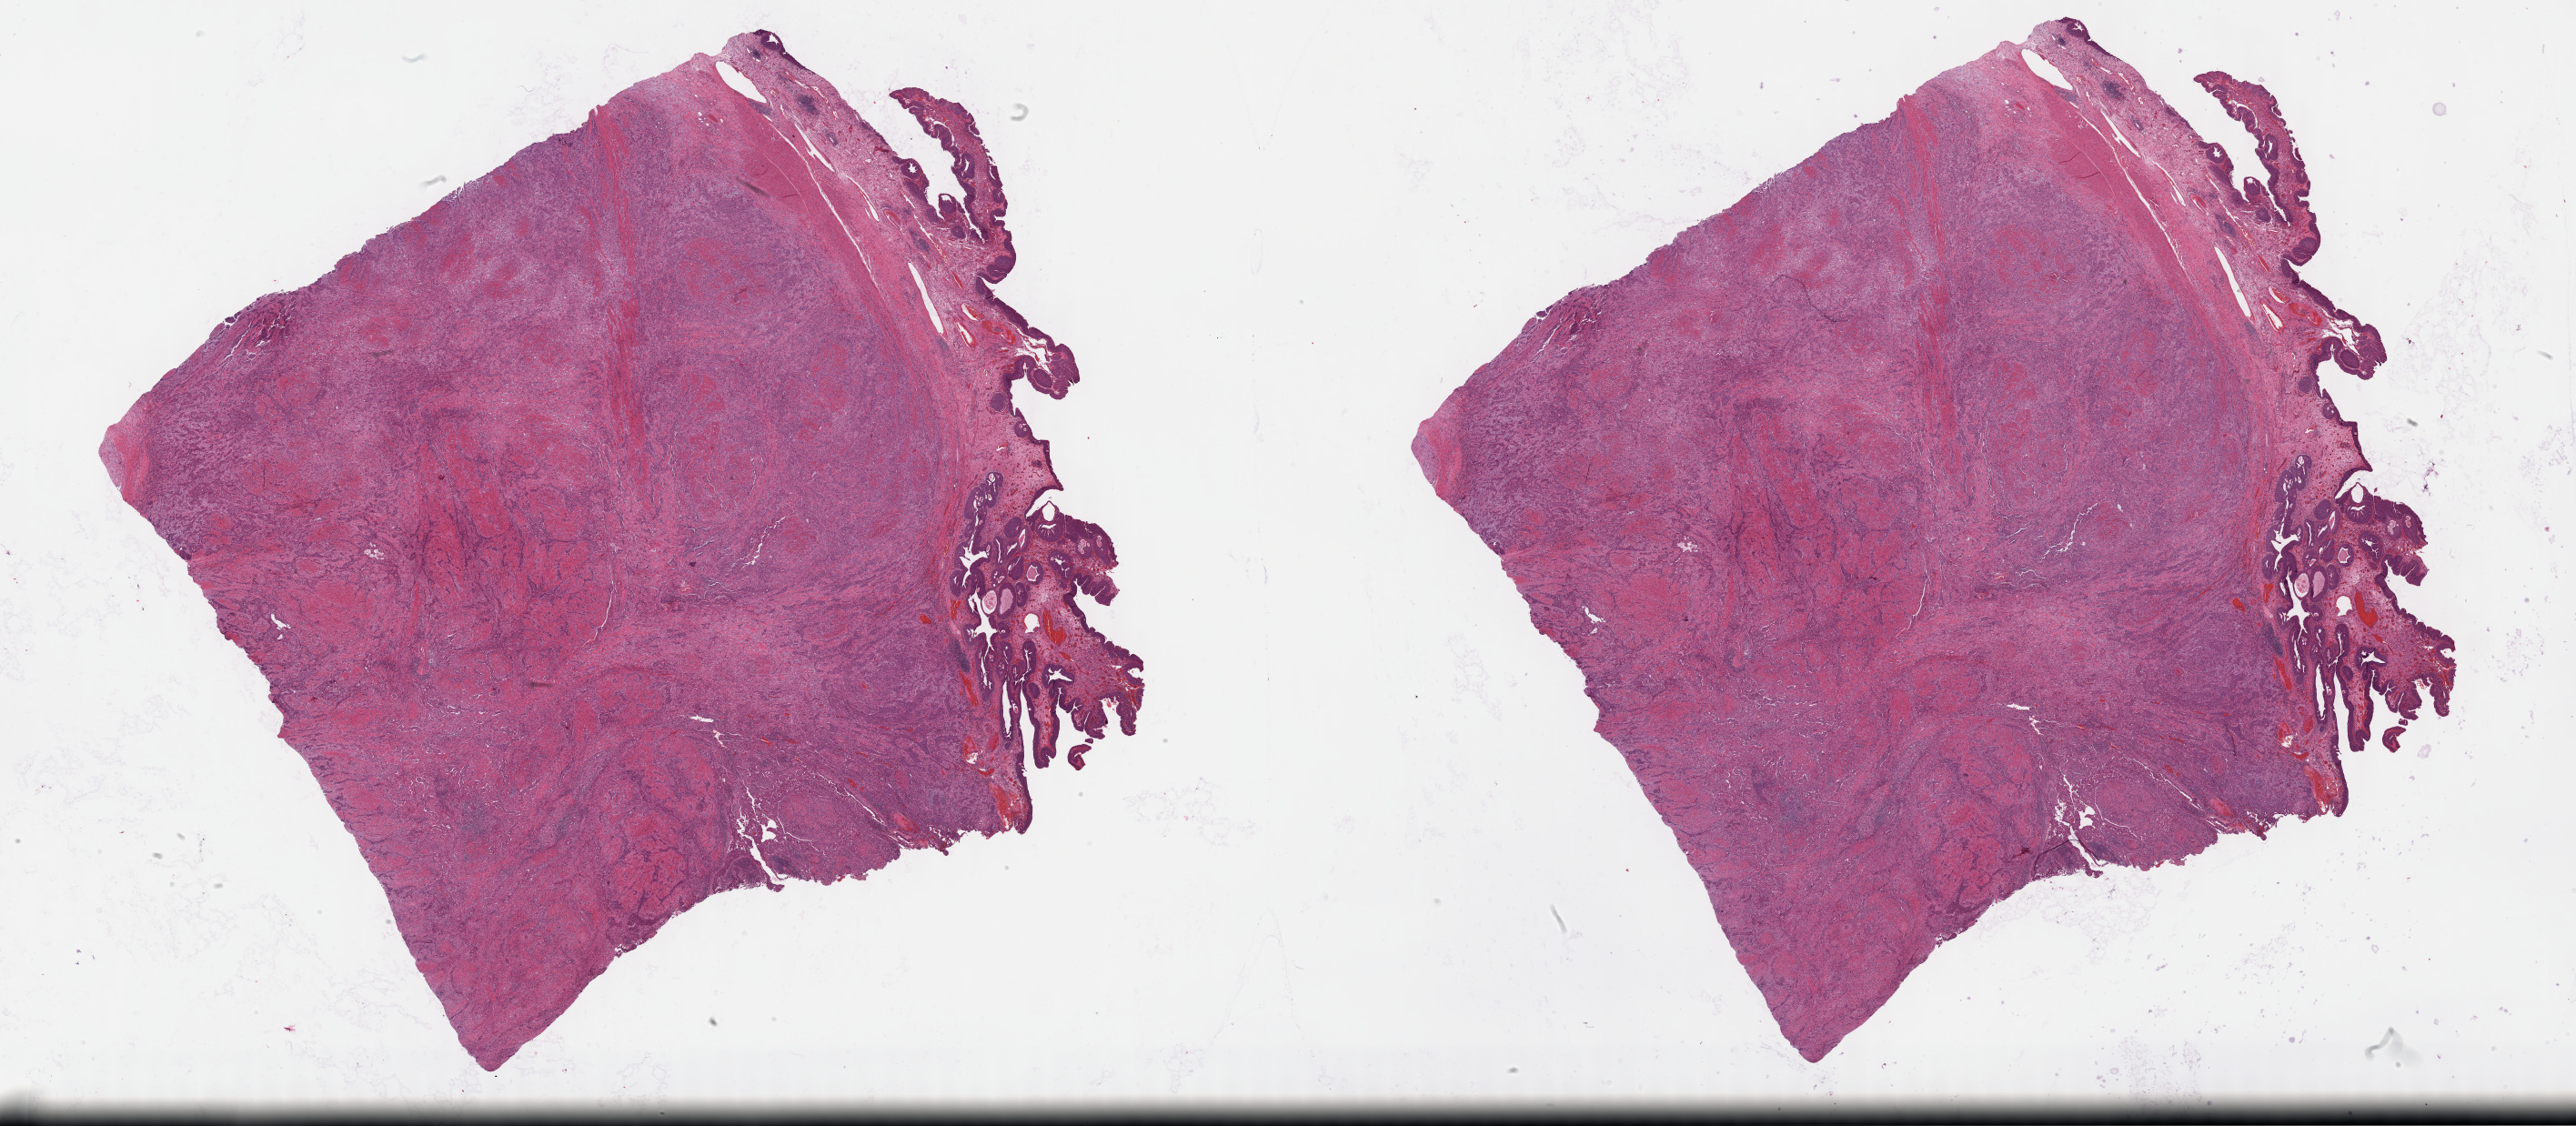
Whole-slide histology image, H&E — a low-resolution overview of the entire scanned area, about 45.8 x 20.0 mm (from a 40x scan); formalin-fixed paraffin-embedded (FFPE) diagnostic section; primary tumour sample from the bladder. Male patient; age at initial diagnosis 77 years. Histologic grade: high grade.
AJCC pathologic stage: III (7th edition). Lymph nodes positive (case pathology): 0 of 34 examined. Histologic diagnosis: Transitional cell carcinoma (anterior wall of bladder).